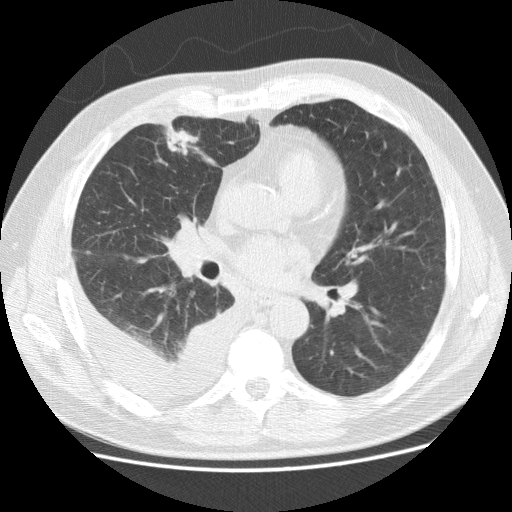
Low-dose screening chest CT, one axial slice; slice 65 of 142 in the series (ordered by position); reconstruction kernel STANDARD; 120 kVp; lung window (W 1500 / L -600 HU); 512 × 512 image matrix, field of view 380 × 380 mm.
Outlined on this slice (expert manual segmentation):
- lesion 1 (tumor, middle lobe of right lung): bounding box (x1, y1, x2, y2) in pixels: (164, 126, 199, 155)